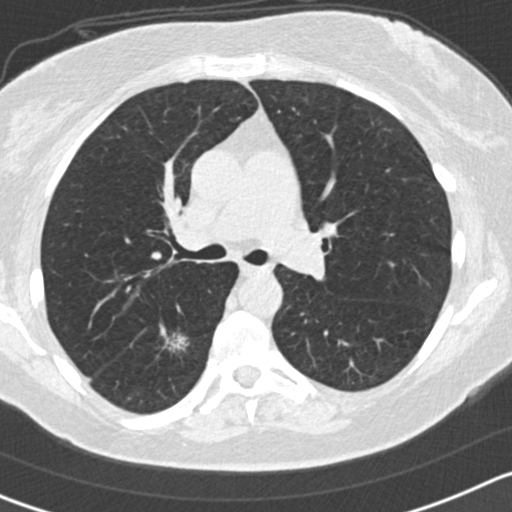
Chest CT (low-dose screening protocol), one axial image; first (baseline) screen; lung window (W 1500 / L -600 HU); 2 mm slice thickness; 120 kVp; slice 62 of 161 in the series; 512 × 512 image matrix, field of view 306 × 306 mm. Female participant, aged 65 years at enrolment. Former smoker at enrolment.
- Expert-annotated lung lesion, bounding box [x1, y1, x2, y2] px = [139, 316, 198, 372].
- Reader record for this screening exam (exam-level; its link to the box is not recorded): non-calcified nodule or mass ≥4 mm, right lower lobe, 14 × 13 mm, spiculated (stellate) margins, mixed attenuation.
- Official screen result: positive, change unspecified: nodule(s) >= 4 mm or enlarging nodule(s), mass(es), or other non-specific abnormalities suspicious for lung cancer.